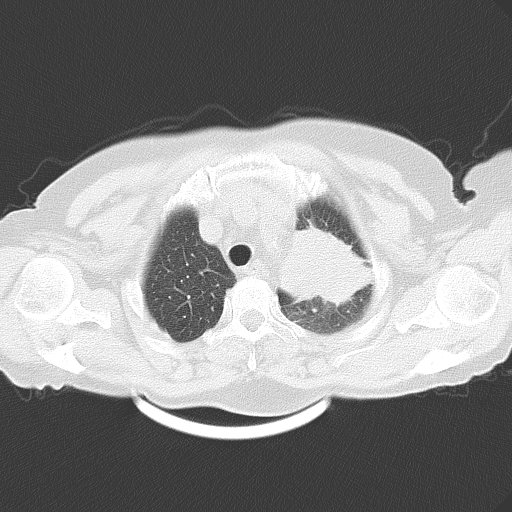
Chest CT, one axial slice. Slice 45 of 54 in the series (ordered by position). Reconstruction kernel B70f. 120 kVp. Lung window (W 1500 / L -600 HU). 5 mm slice thickness. 512 × 512 image matrix, field of view 353 × 353 mm. Patient: female, 71 years. Case-level facts recorded for this patient, not image findings: clinical TNM (as recorded): T3 N3 M0.
Outlined on this slice (bounding box drawn by a radiologist):
- lung tumour (recorded histology: adenocarcinoma): bounding box <269,218,378,318> (left, top, right, bottom; pixels)